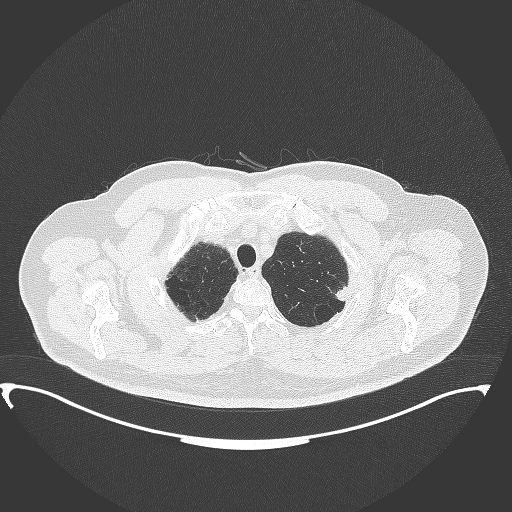
Chest CT, one axial slice; slice 327 of 350 in the series (ordered by position); lung window (W 1500 / L -600 HU); 1 mm slice thickness; 512 × 512 image matrix, field of view 459 × 459 mm. Patient: male, 64 years. Case-level facts recorded for this patient, not image findings: clinical TNM (as recorded): T1c N1 M1.
Annotated regions visible in this slice (bounding box drawn by a radiologist):
- lung tumour (recorded histology: adenocarcinoma): bounding box <332,282,357,303> (left, top, right, bottom; pixels)